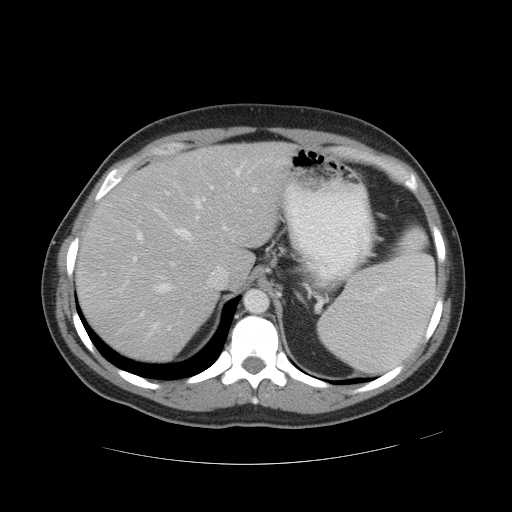
Contrast-enhanced abdominal CT, one axial slice; reconstruction kernel STANDARD; 120 kVp; intravenous contrast given; soft-tissue window (W 400 / L 40 HU); 5 mm slice thickness; 512 × 512 image matrix, field of view 422 × 422 mm. Male patient, age 42 years. From the clinical record (not read from this slice): diagnosis: colorectal cancer liver metastases, imaged before liver resection; multiple liver metastases: yes; largest metastasis: 2.8 cm; disease in both lobes: yes.
Annotated regions visible in this slice (expert manual segmentation):
- hepatic veins: bounding box [x1, y1, x2, y2] px = [152, 163, 245, 329]
- liver: [78, 143, 288, 361]
- planned liver remnant (the part of the liver to remain after resection): [78, 143, 288, 361]
- portal vein (with intrahepatic branches): [132, 182, 257, 317]